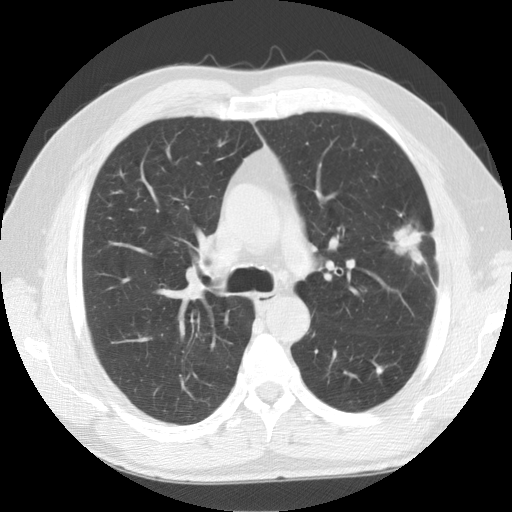
Low-dose screening chest CT, one axial slice; position 96 of 141 along the scan axis; 120 kVp; lung window (W 1500 / L -600 HU); 512 × 512 image matrix.
Annotated regions visible in this slice (manually delineated by an expert):
- lesion 1 (tumor, upper lobe of left lung): bounding box [x1, y1, x2, y2] px = [393, 224, 425, 265]